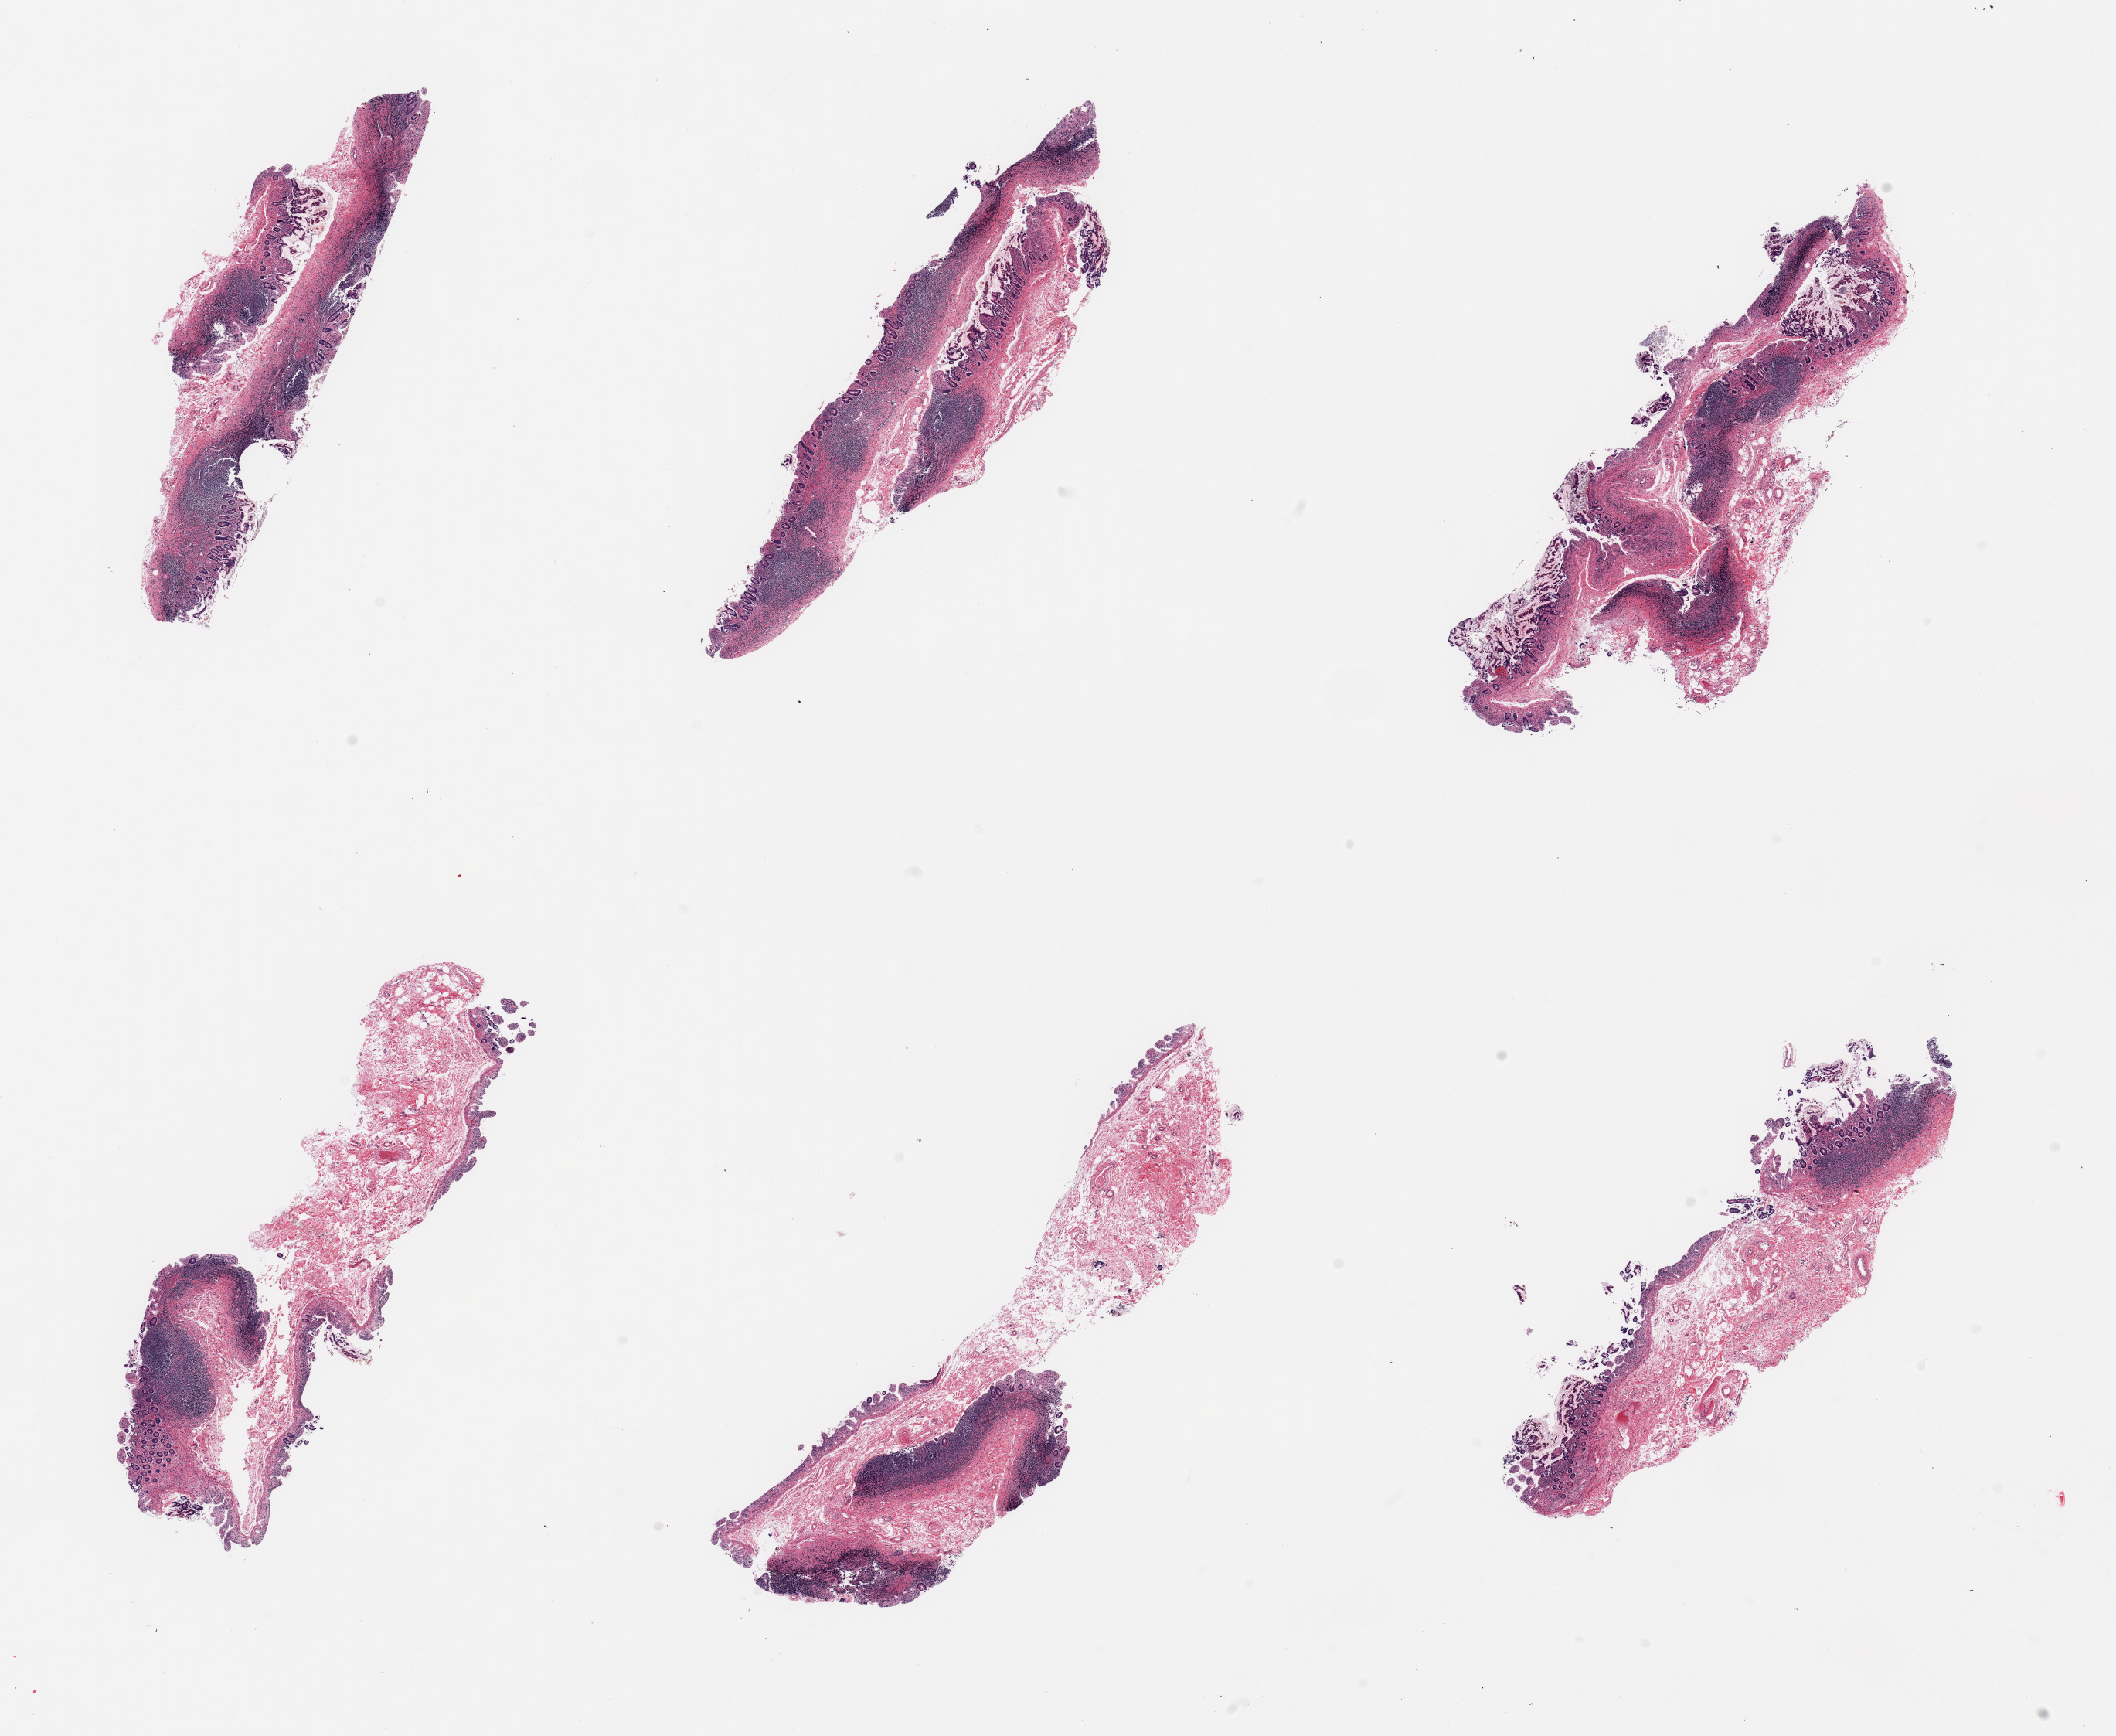
Haematoxylin and eosin whole-slide image, low-resolution overview of the scanned area, about 21.7 x 17.8 mm (slide scanned at 20x), PAXgene-fixed paraffin-embedded (PFPE) section, sampled site (target tissue): ileum, donor tissue sample. Male donor.
Review note (as recorded): 6 pieces; moderately and focally severely autolyzed mucosa; well representaion of target lymphoid aggregates.